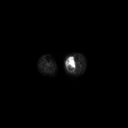
FDG PET of an extremity soft-tissue mass (from a PET/CT study), one axial slice; slice 138 of 223 in the series (ordered by position); 128 × 128 image matrix. Patient: female, 70 years. Case-level facts recorded for this patient, not image findings: histological type: extraskeletal high grade osteogenic sarcoma; grade: high; site of the primary tumour: left calf.
Outlined on this slice (expert contour drawn on MRI and transferred to this co-registered scan by the dataset authors):
- gross tumour volume (mass): bounding box (x1, y1, x2, y2) in pixels: (66, 58, 75, 70)